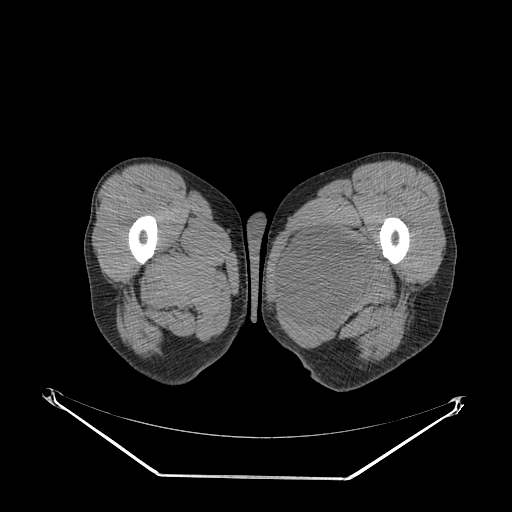
CT of an extremity soft-tissue mass (from a PET/CT study), one axial slice; slice 31 of 267 in the series (ordered by position); soft-tissue window (W 400 / L 40 HU); 512 × 512 image matrix, field of view 500 × 500 mm. Male patient. Case-level facts recorded for this patient, not image findings: histological type: pleiomorphic liposarcoma; grade: high; site of the primary tumour: left thigh.
Annotated regions visible in this slice (expert contour drawn on MRI and transferred to this co-registered scan by the dataset authors):
- gross tumour volume including surrounding oedema: bounding box (x1, y1, x2, y2) in pixels: (283, 226, 380, 323)
- gross tumour volume (mass): (285, 228, 378, 314)